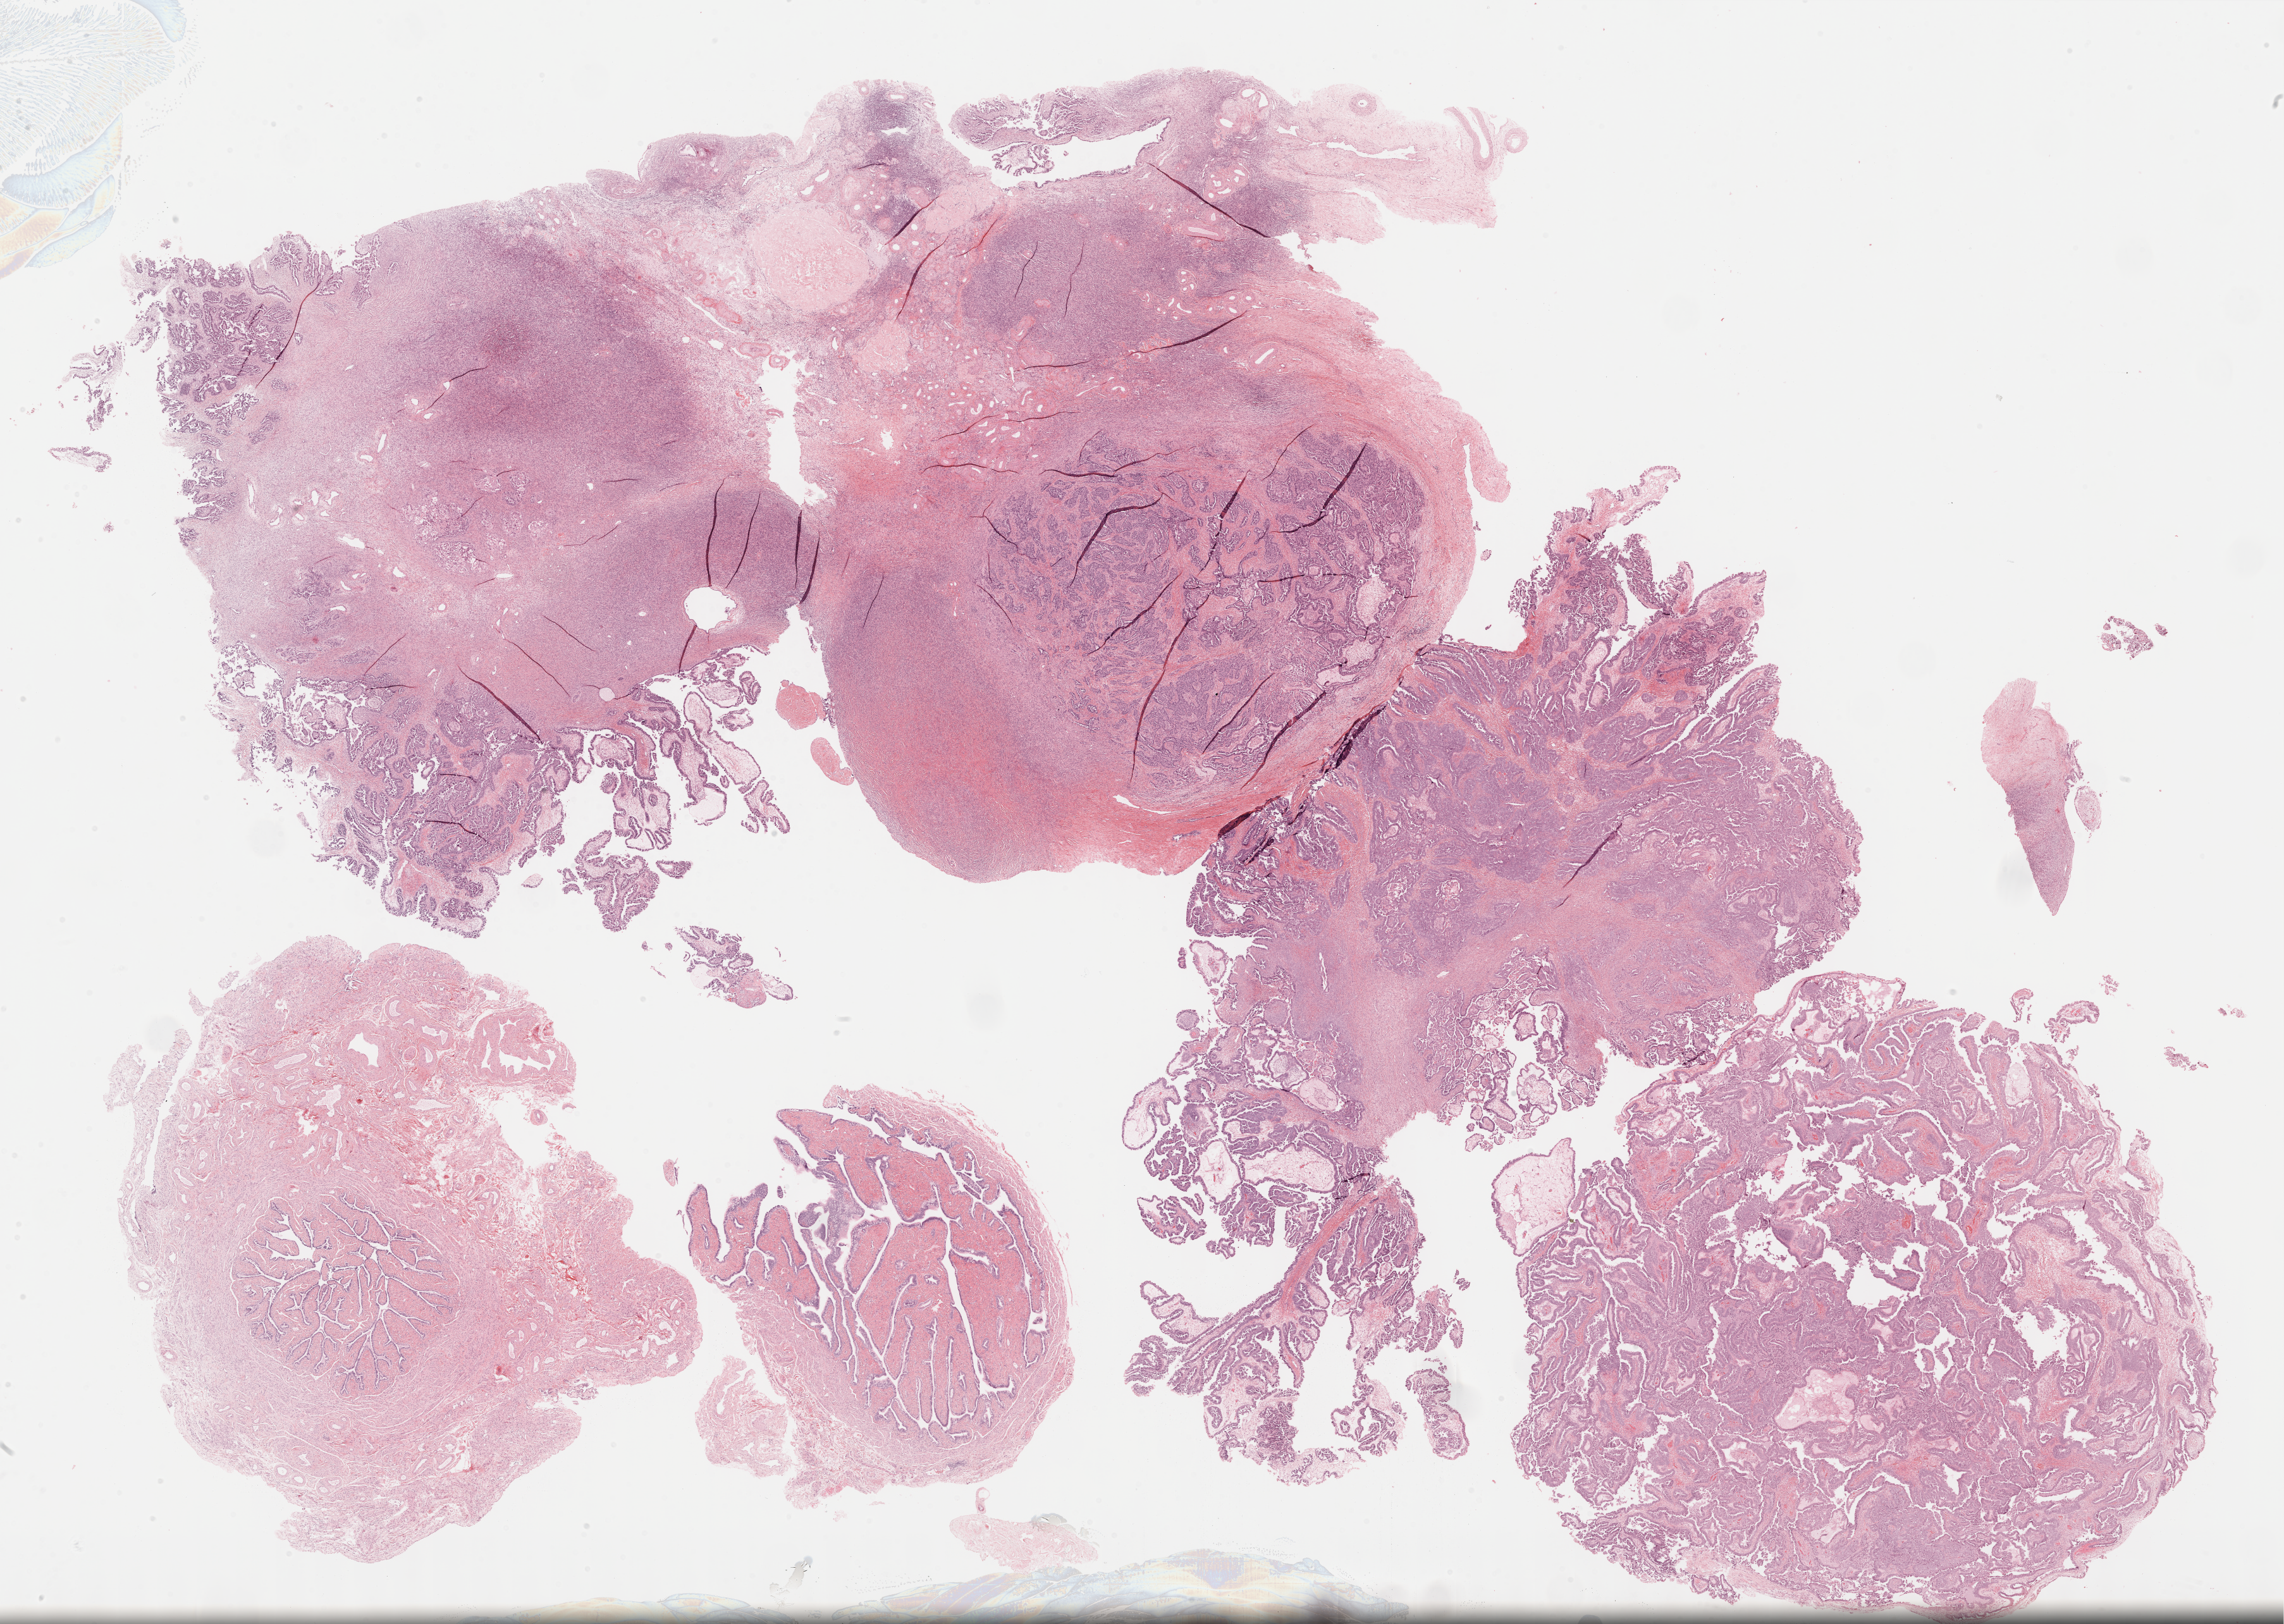
Digitized Hematoxylin and eosin (H&E) stained tissue section (whole slide) — a low-resolution overview of the entire scanned area, about 29.2 x 20.7 mm; FFPE section; ovary, primary tumour sample. Patient: female, age at initial diagnosis 75 years. Histologic grade: G3 (poorly differentiated).
Laterality: bilateral. FIGO stage: IIIC. Diagnosis: Serous cystadenocarcinoma, NOS.